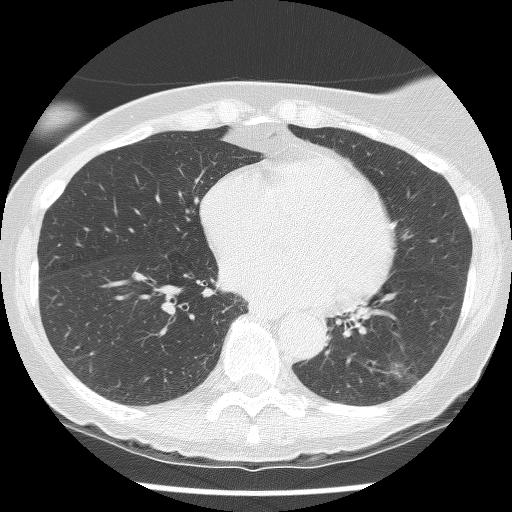
Low-dose screening chest CT, axial slice. Second screening round (one year after baseline). Lung window (W 1500 / L -600 HU). 2.5 mm slice thickness. Female participant, aged 61 years at enrolment. Current smoker at enrolment.
Expert-annotated lung lesion, bounding box <335,337,435,420> (left, top, right, bottom; pixels). The screening reader recorded 2 non-calcified nodules or masses ≥4 mm on this exam (left lower lobe, left lower lobe); which of them this box marks is not recorded. Later outcome: lung cancer diagnosed 585 days after this screen (after the third annual screen) — non-small cell carcinoma, left lower lobe, poorly differentiated (G3), stage IB (AJCC 6th edition), 100 mm at pathology.